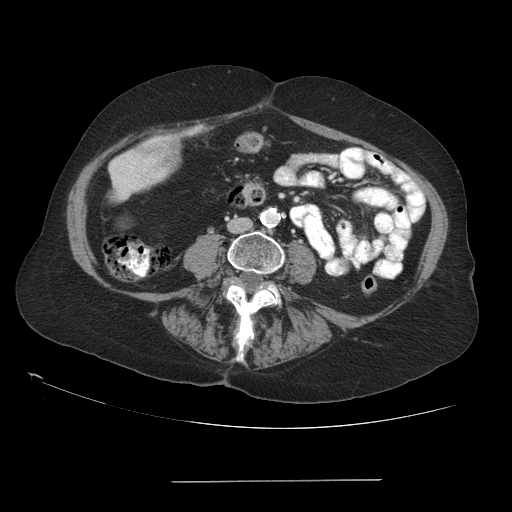
Contrast-enhanced abdominal CT (liver protocol), one axial slice; slice 13 of 89 in the series (ordered by position); 140 kVp; soft-tissue window (W 400 / L 40 HU); 512 × 512 image matrix, field of view 400 × 400 mm. Case-level facts recorded for this patient, not image findings: diagnosis: hepatocellular carcinoma (patient treated with transarterial chemoembolisation; whether this scan precedes or follows treatment is not stated here); TNM stage (as recorded): Stage-IVA; Child-Pugh class: A.
Annotated regions visible in this slice (semi-automatically segmented with operator editing):
- mass: bounding box (x1, y1, x2, y2) in pixels: (138, 138, 179, 170)